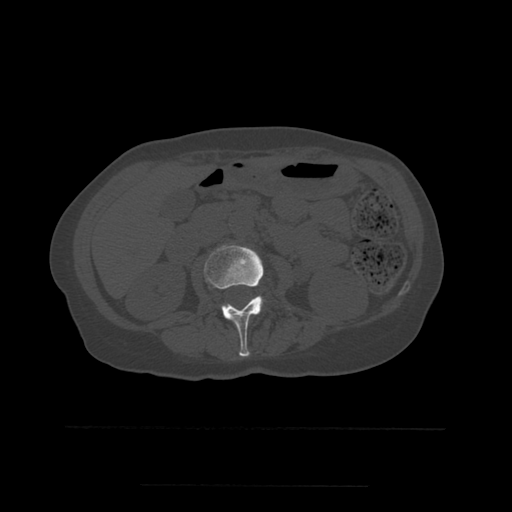
CT including the spine, one axial slice. Position 207 of 544 along the scan axis. Bone window (W 1800 / L 400 HU). 512 × 512 image matrix, field of view 350 × 350 mm. Patient age 58 years. From the clinical record (not read from this slice): primary cancer: lung.
Outlined on this slice (semi-automatically segmented with operator editing):
- L2 vertebra: box from (x=204, y=245) to (x=266, y=357) px